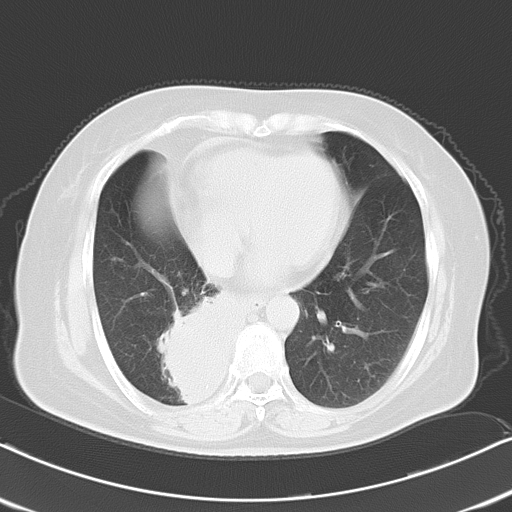
Chest CT, one axial slice; position 7 of 21 along the scan axis; reconstruction kernel B70f; 120 kVp; lung window (W 1500 / L -600 HU); 10 mm slice thickness; 512 × 512 image matrix. Female patient, age 61 years. Case-level facts recorded for this patient, not image findings: clinical TNM (as recorded): T1b N0 M1b.
Outlined on this slice (rectangle marked by the reading radiologist):
- lung tumour (recorded histology: squamous cell carcinoma): bounding box (x1, y1, x2, y2) in pixels: (165, 295, 260, 415)